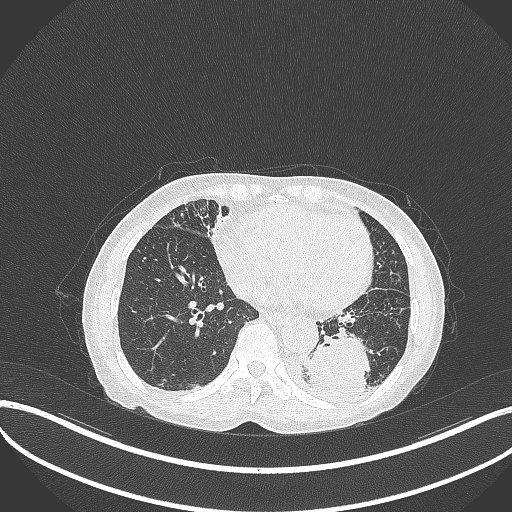
Chest CT, one axial slice. Position 101 of 370 along the scan axis. Reconstruction kernel B70f. Lung window (W 1500 / L -600 HU). 1 mm slice thickness. 512 × 512 image matrix, field of view 400 × 400 mm. Patient: female, 78 years. From the clinical record (not read from this slice): clinical TNM (as recorded): T3 N0 M1.
Structures marked on this image (rectangle marked by the reading radiologist):
- lung tumour (recorded histology: squamous cell carcinoma): box from (x=303, y=334) to (x=372, y=402) px